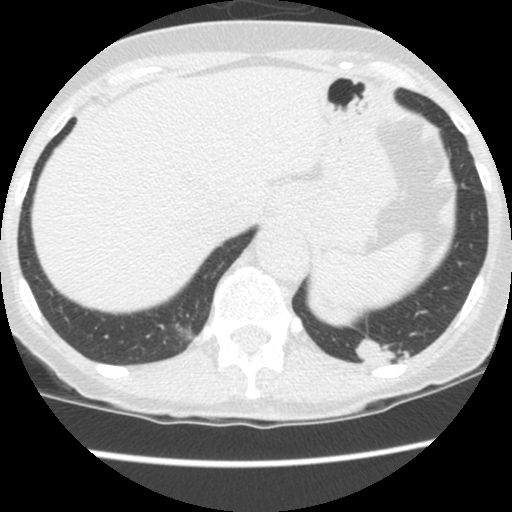
Low-dose screening chest CT, one axial slice; slice 24 of 130 in the series (ordered by position); 120 kVp; lung window (W 1500 / L -600 HU); 2.5 mm slice thickness; 512 × 512 image matrix, field of view 290 × 290 mm.
Outlined on this slice (manually delineated by an expert):
- lesion 1 (tumor, lower lobe of left lung): bounding box [x1, y1, x2, y2] px = [355, 337, 412, 364]